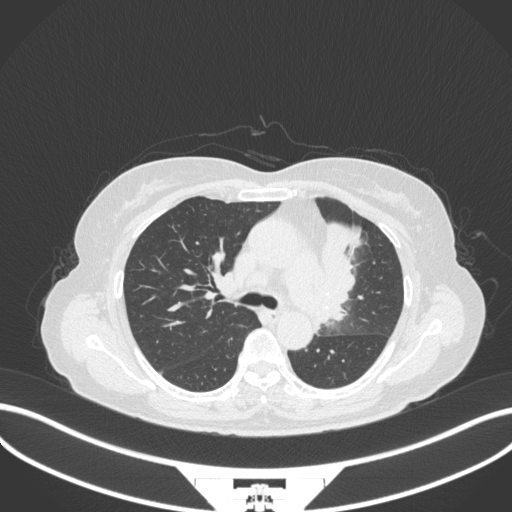
Chest CT, one axial slice; slice 218 of 382 in the series (ordered by position); lung window (W 1500 / L -600 HU); 1 mm slice thickness; 512 × 512 image matrix, field of view 400 × 400 mm. Female patient, age 64 years. Case-level facts recorded for this patient, not image findings: clinical TNM (as recorded): T2a N2 M0.
Annotated regions visible in this slice (bounding box drawn by a radiologist):
- lung tumour (recorded histology: adenocarcinoma): bounding box (x1, y1, x2, y2) in pixels: (322, 218, 365, 321)